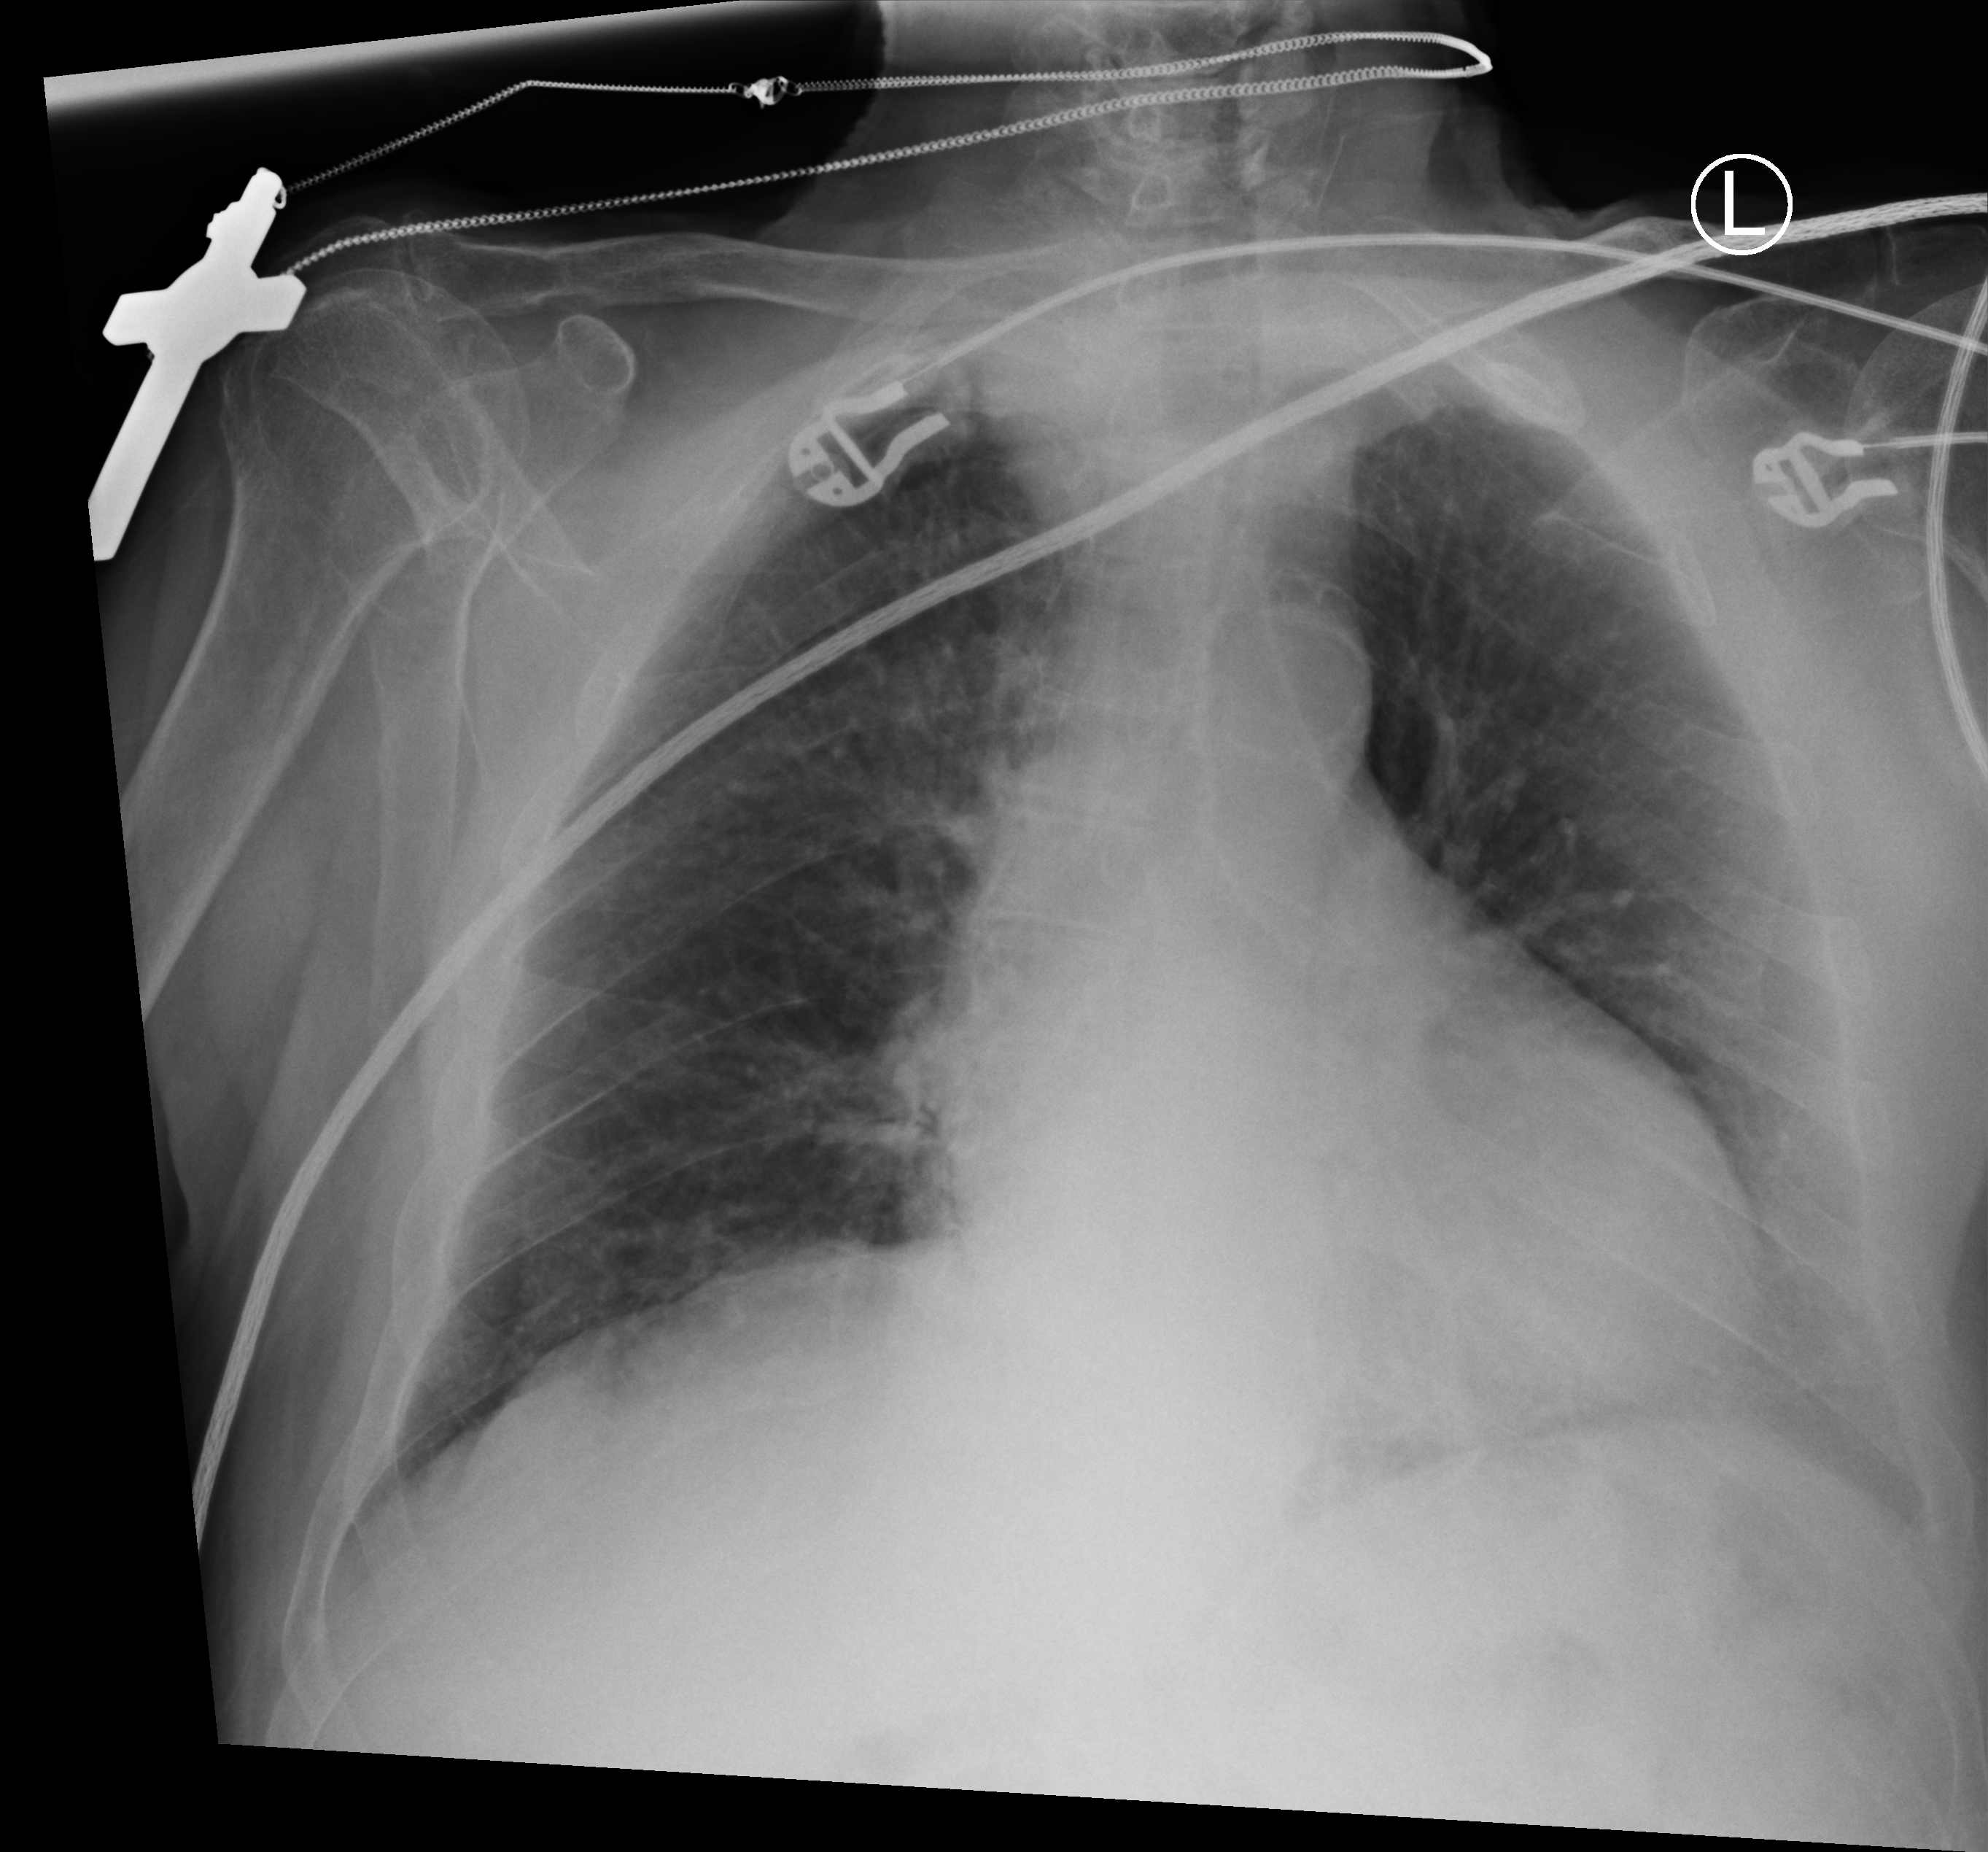
Bedside chest radiograph (computed radiography); anteroposterior (AP) projection. Patient hospitalised with COVID-19; male, aged 75–90 years.
Hospital-stay facts (about this admission, not read from this image; timing relative to this image not recorded): COPD (admission record): no; length of hospital stay: 14 days.